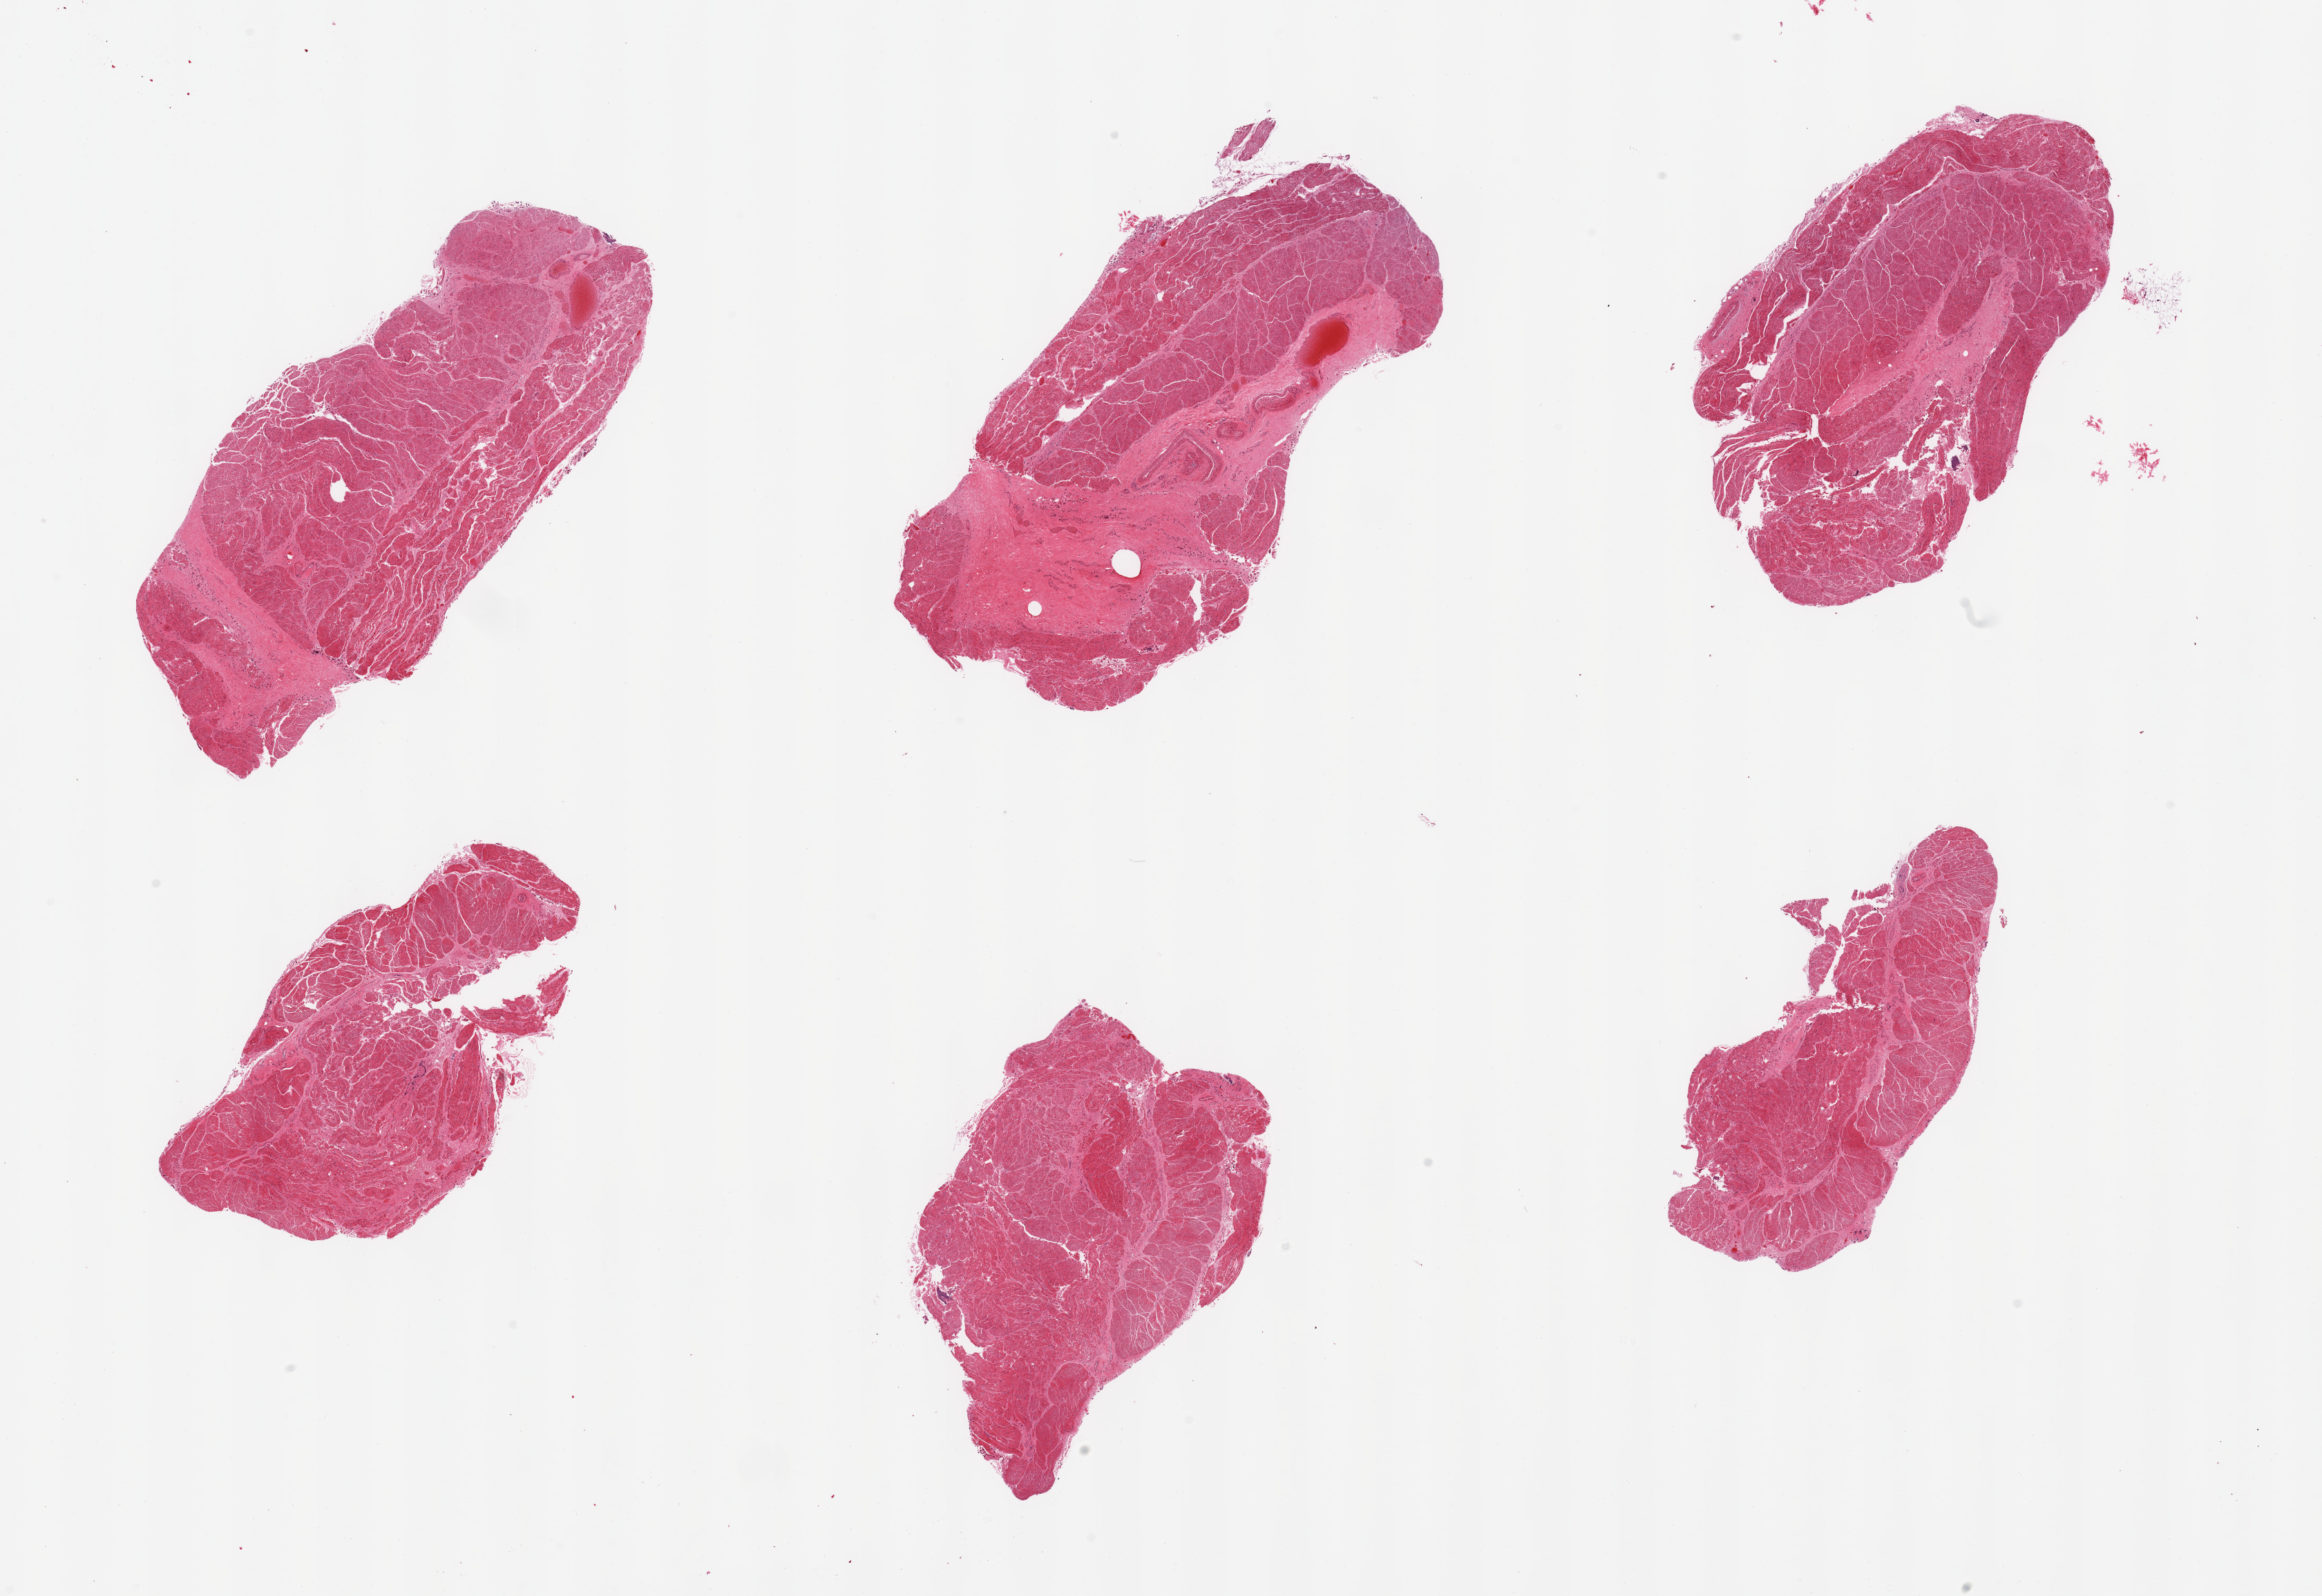
H&E whole-slide image, brightfield, low-resolution overview of the scanned area, about 26.6 x 18.3 mm (from a 20x scan). PAXgene-fixed paraffin-embedded (PFPE) section. Sampled site (target tissue): gastroesophageal junction. Tissue donor sample. Donor: male.
Review note (as recorded): 6 pieces; up to 40% fibrous content.